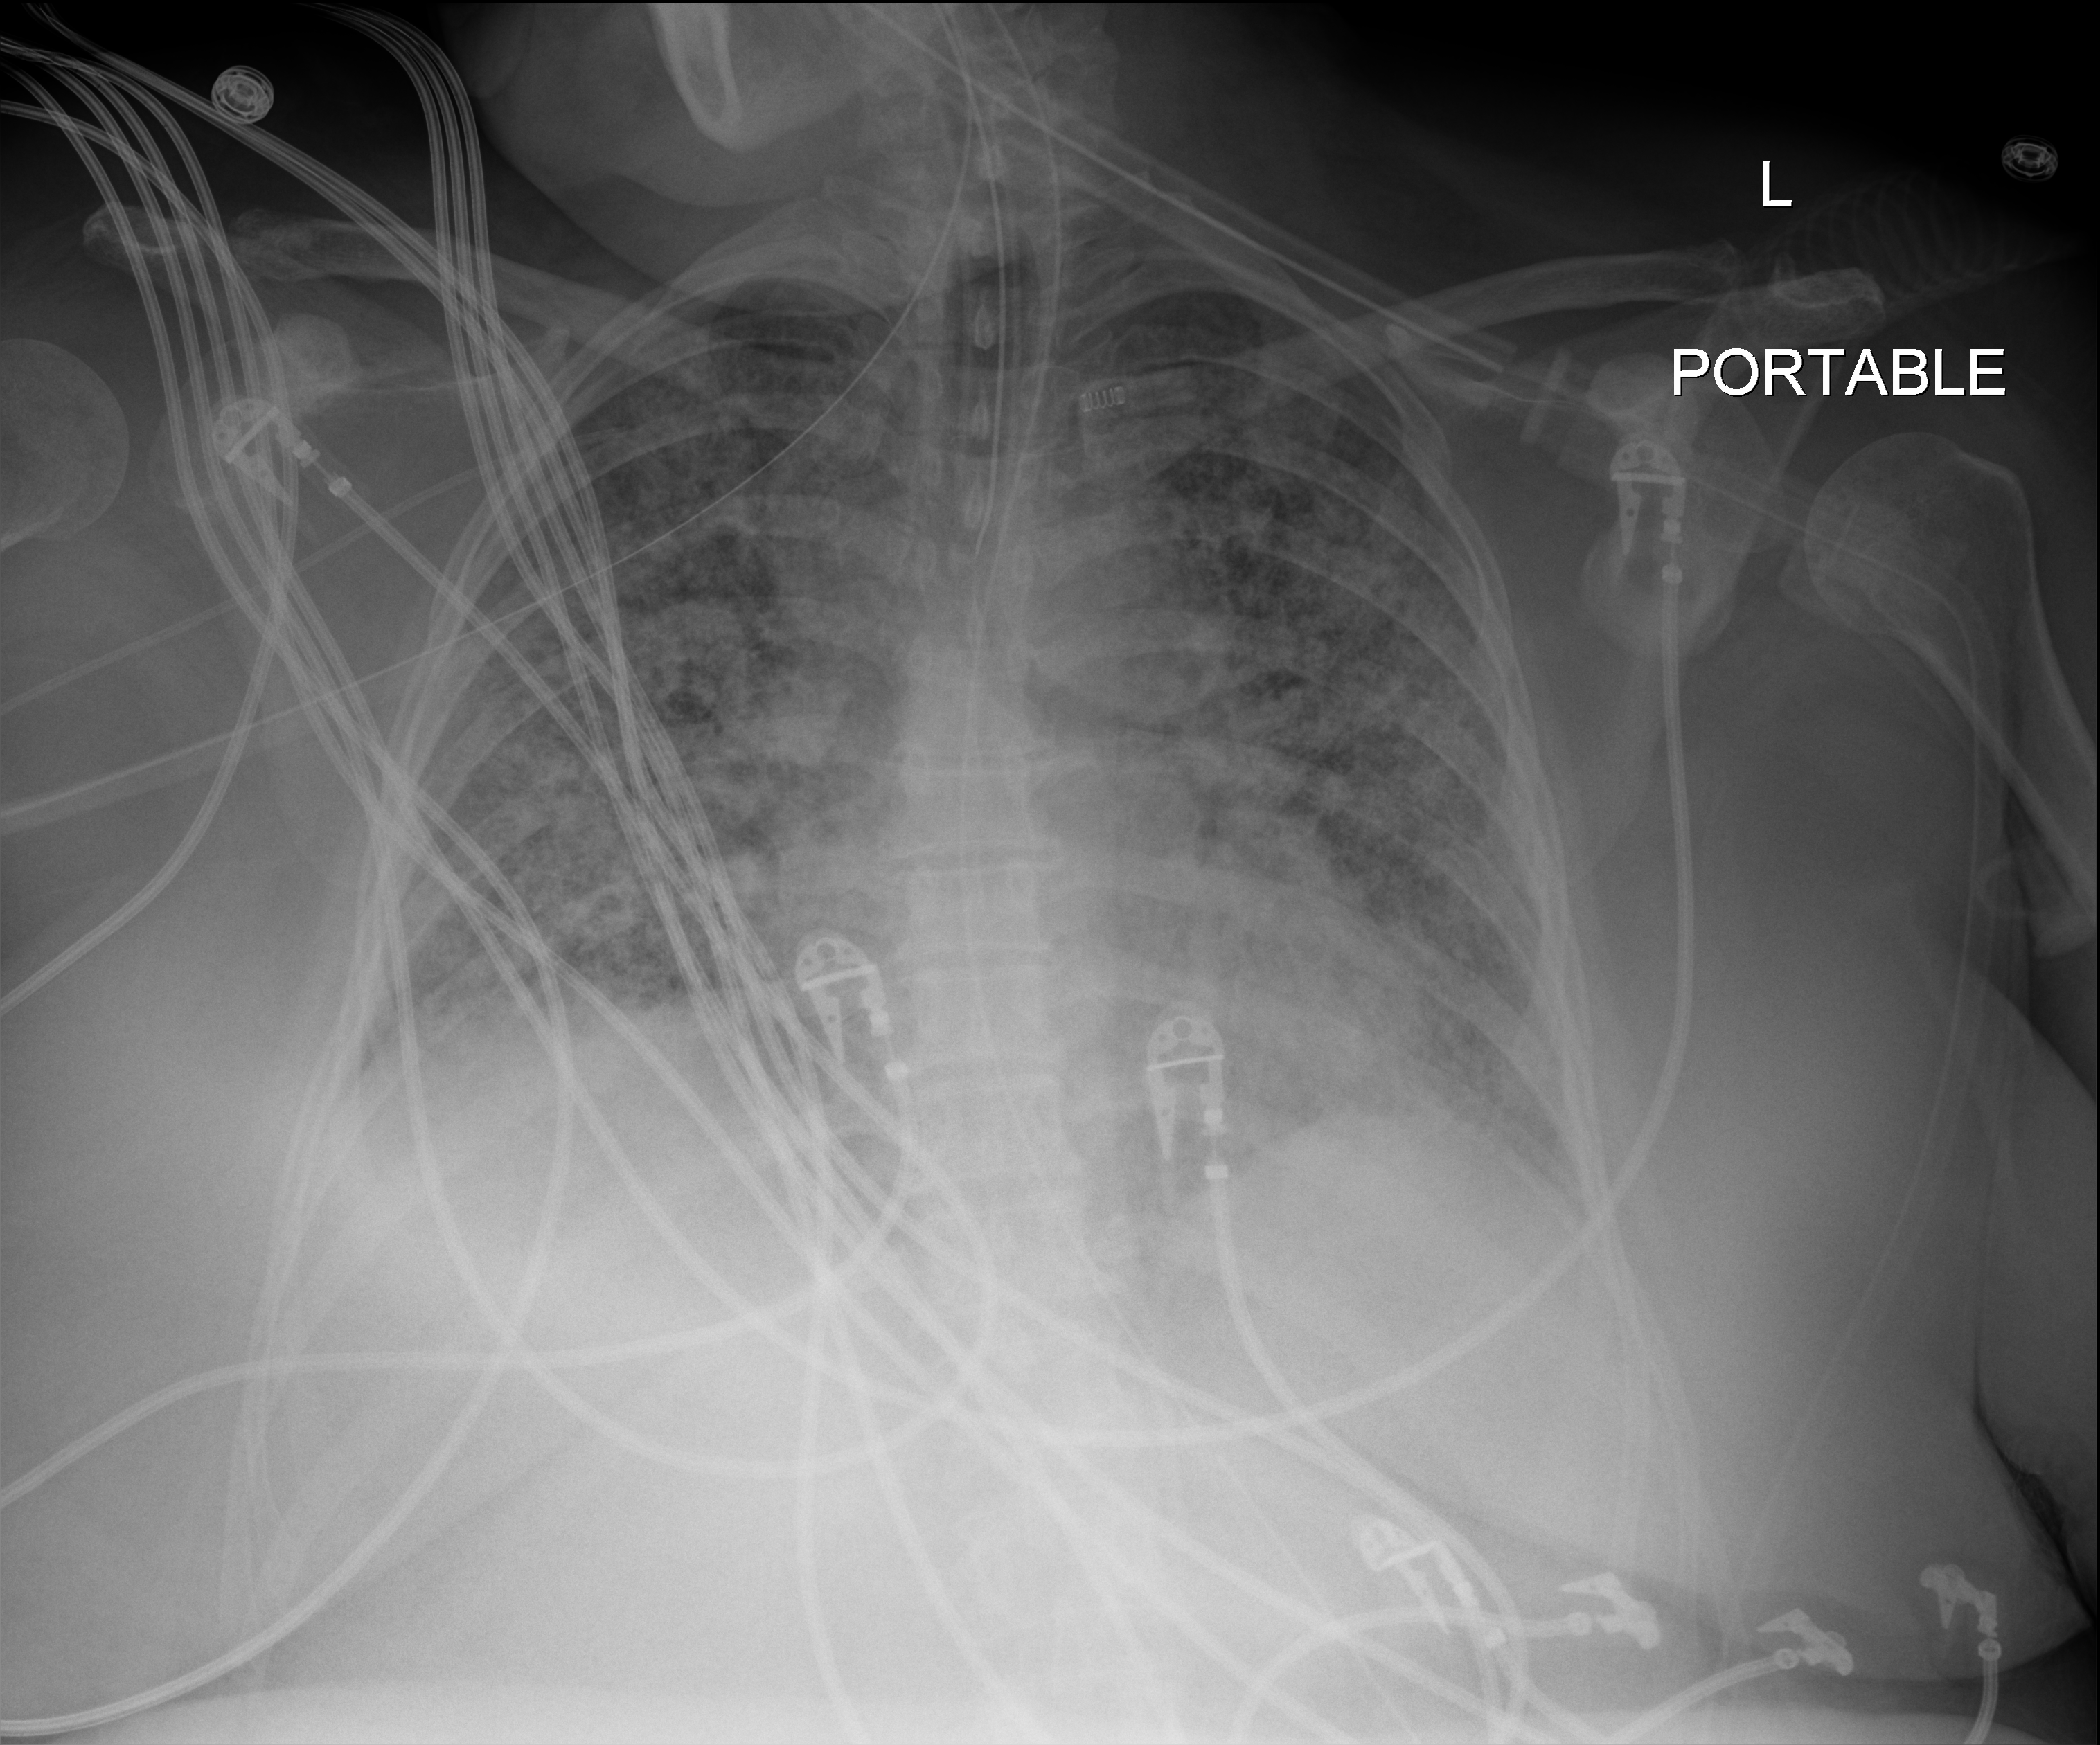
Portable chest radiograph, anteroposterior (AP) projection. Patient hospitalised with COVID-19; female, aged 18–59 years.
Admission-level facts for this patient (not findings on this image; timing relative to this image not recorded):
- mechanically ventilated during this hospital stay: yes
- chronic kidney disease (admission record): no